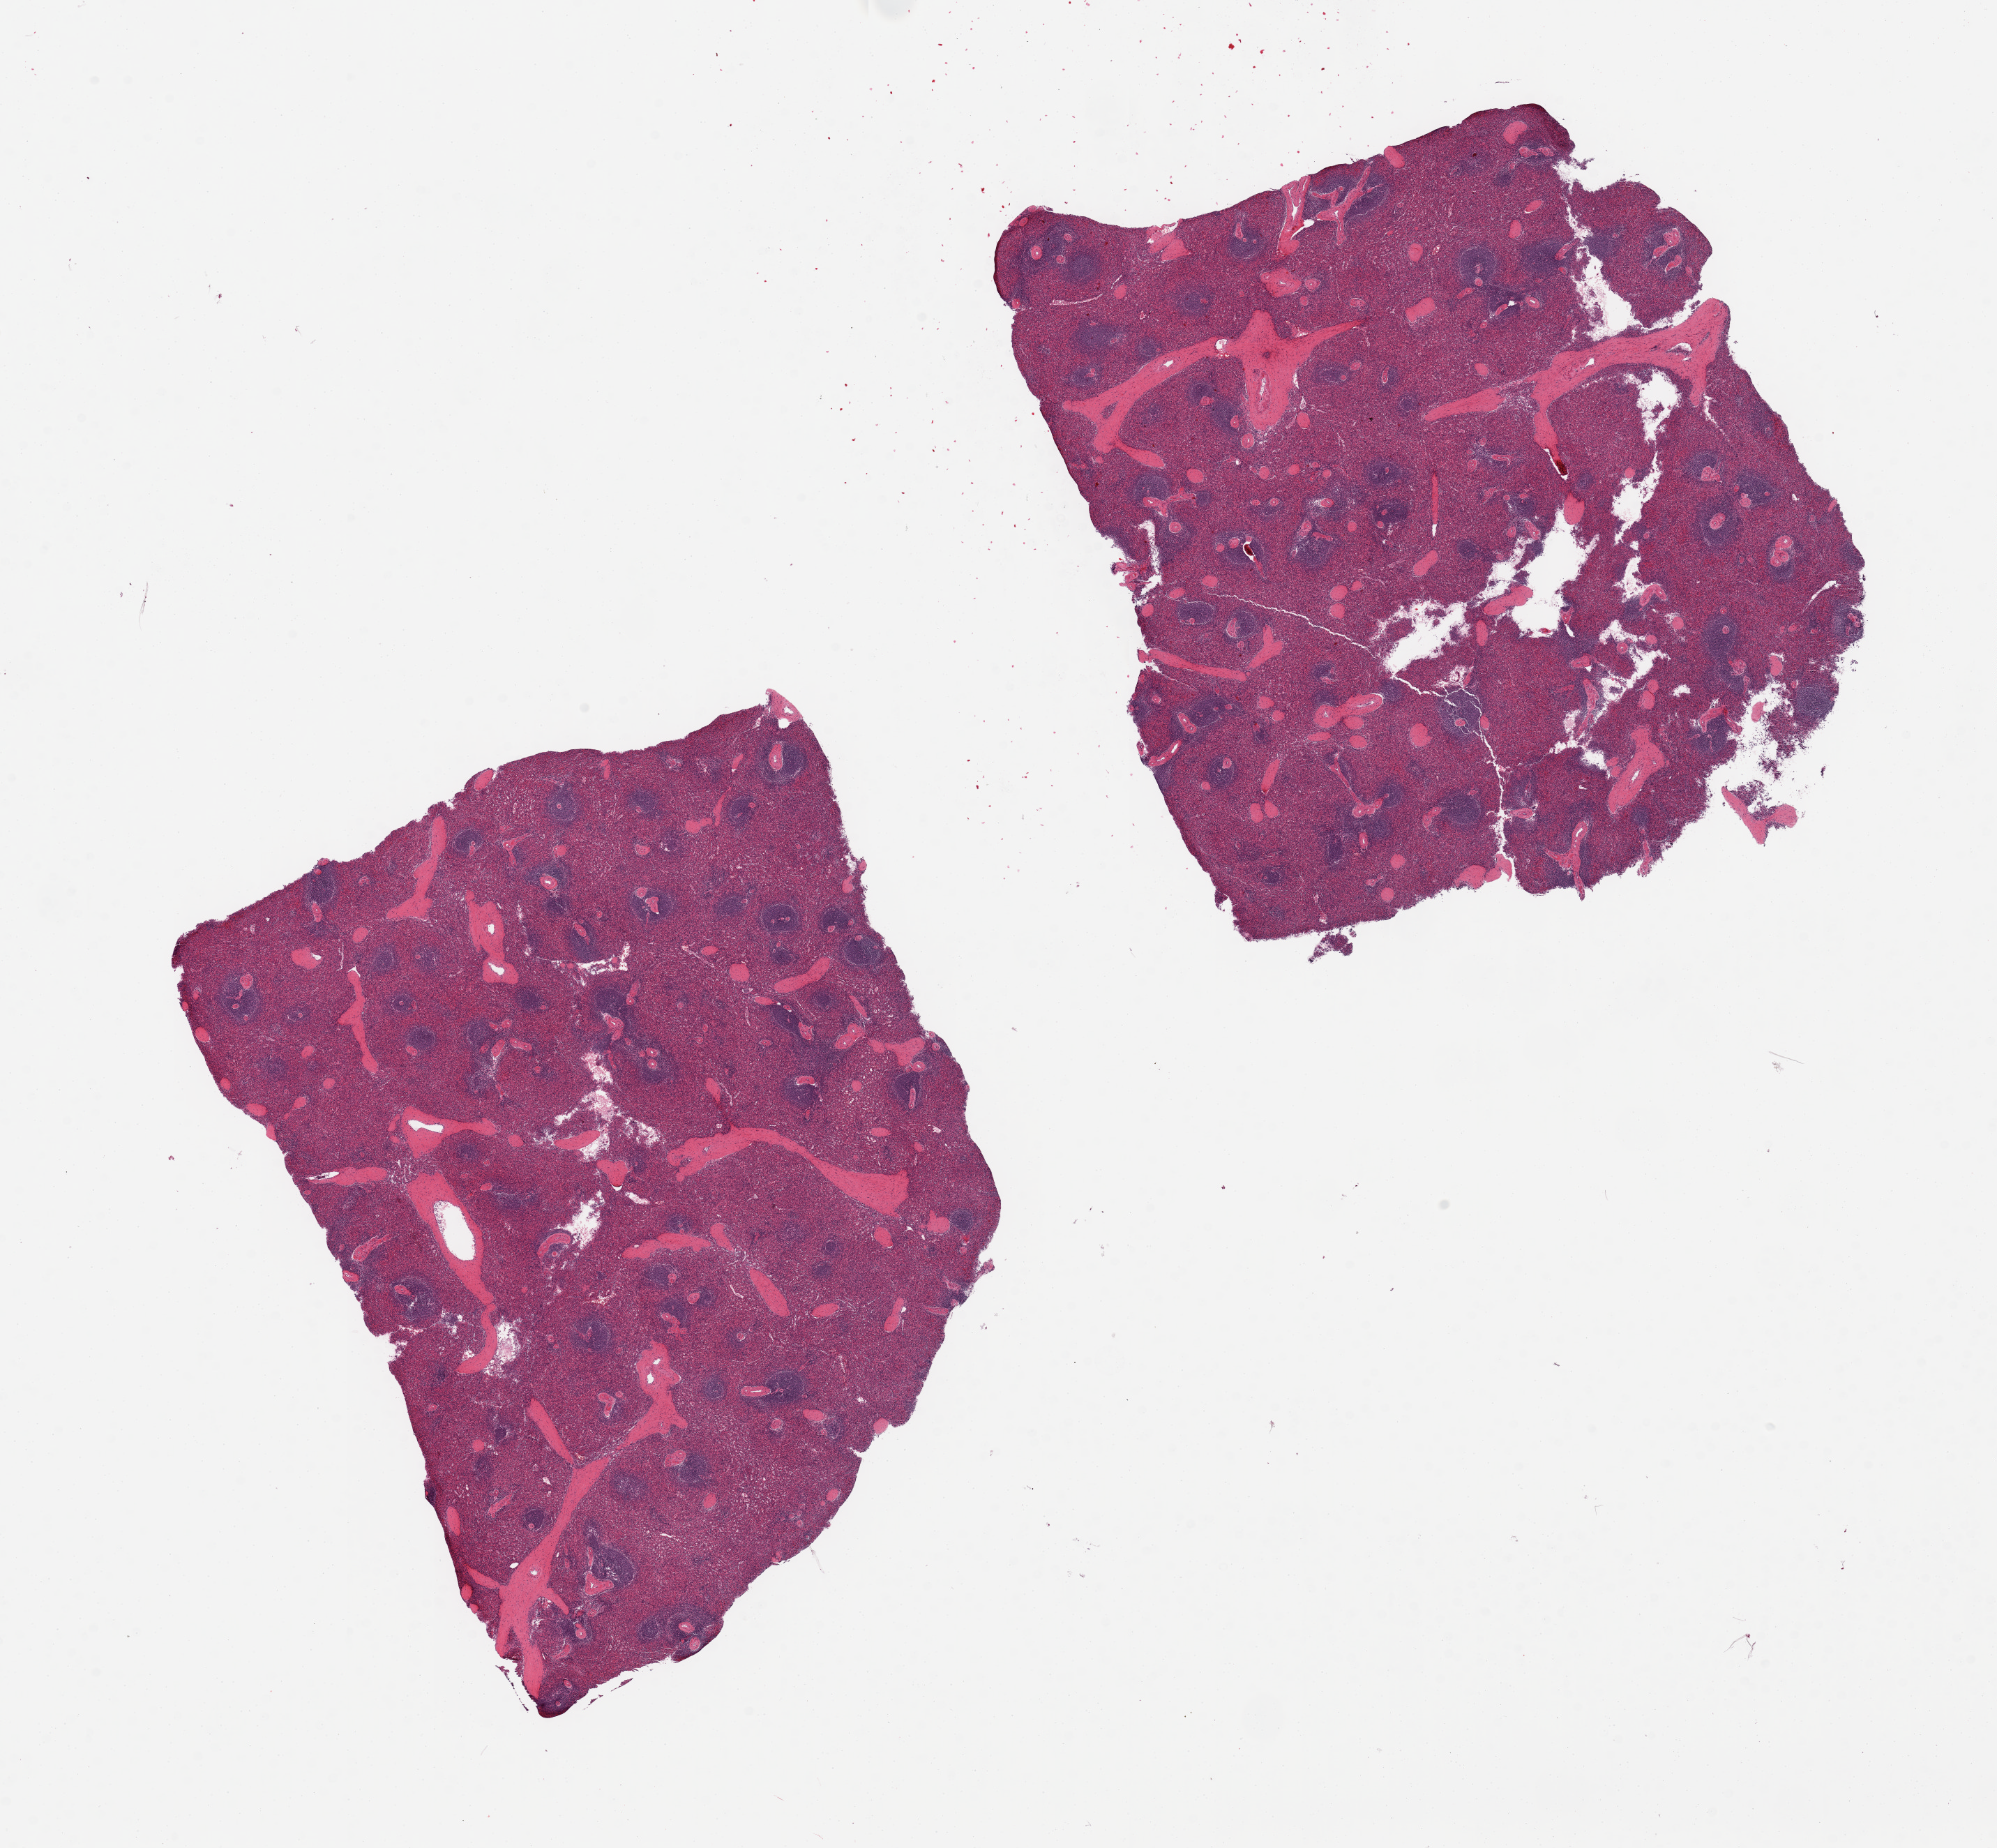
Digitized haematoxylin and eosin-stained section — whole scanned area (about 22.6 x 20.9 mm) shown as a low-resolution overview, PAXgene-fixed, paraffin-embedded tissue, sampled site (target tissue): spleen, tissue donor sample. Female donor.
Reviewer comment on this tissue sample: 2 pieces.